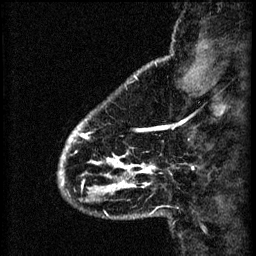
Breast MRI (dynamic contrast-enhanced), one sagittal slice; slice 10 of 60 in the series (ordered by position); 3 images stored at this slice position (order not interpretable as contrast timing); 1.5 T; TE 4.2 ms, TR 8.2 ms; 2.2 mm slice thickness; 256 × 256 image matrix. Patient: female, 41 years.
Structures marked on this image (semi-automatically segmented with operator editing):
- analysis volume of interest (the breast-tissue region the enhancement analysis was run in; not a lesion): bounding box <59,112,155,203> (left, top, right, bottom; pixels)
- tumour enhancement mask (voxels above the 70 % enhancement threshold inside the analysis volume of interest): <59,124,155,193>